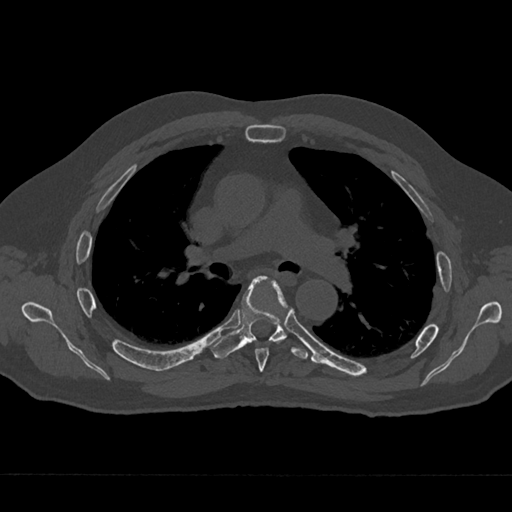
CT including the spine, one axial slice; position 446 of 797 along the scan axis; reconstruction kernel Br40s/3; 120 kVp; bone window (W 1800 / L 400 HU); 512 × 512 image matrix, field of view 377 × 377 mm. Male patient, age 75 years. From the clinical record (not read from this slice): primary cancer: renal; vertebrae with lytic lesions (as recorded): T4.
Annotated regions visible in this slice (semi-automatically segmented with operator editing):
- T5 vertebra: bounding box [x1, y1, x2, y2] px = [255, 281, 288, 372]
- T6 vertebra: [210, 276, 308, 359]